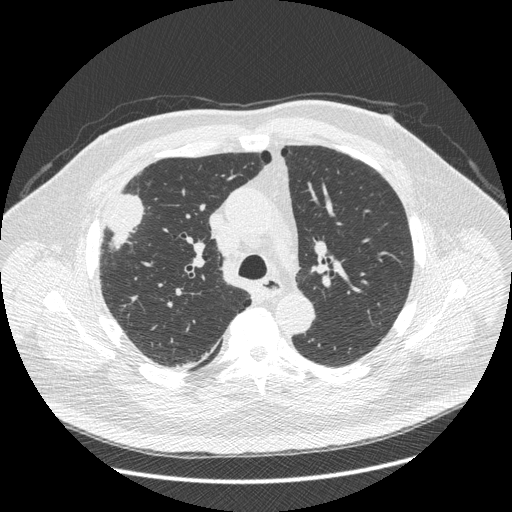
Chest CT (low-dose screening protocol), one axial image. Third screening round (two years after baseline). Lung window (W 1500 / L -600 HU). 1.25 mm slice thickness. 120 kVp. Male participant, aged 66 years at enrolment. Current smoker at enrolment.
• Expert-annotated lung lesion, bounding box (x1, y1, x2, y2) in pixels: (86, 190, 145, 267).
• The exam's reader record, not a measurement of the box and not confirmed to be the same lesion: non-calcified nodule or mass ≥4 mm, right upper lobe, 48 × 25 mm, spiculated (stellate) margins, soft tissue attenuation, pre-existing on the prior screen: no.
• Lung cancer was diagnosed 35 days after this screen: non-small cell carcinoma, right upper lobe, stage IV (AJCC 6th edition), 50 mm at pathology.